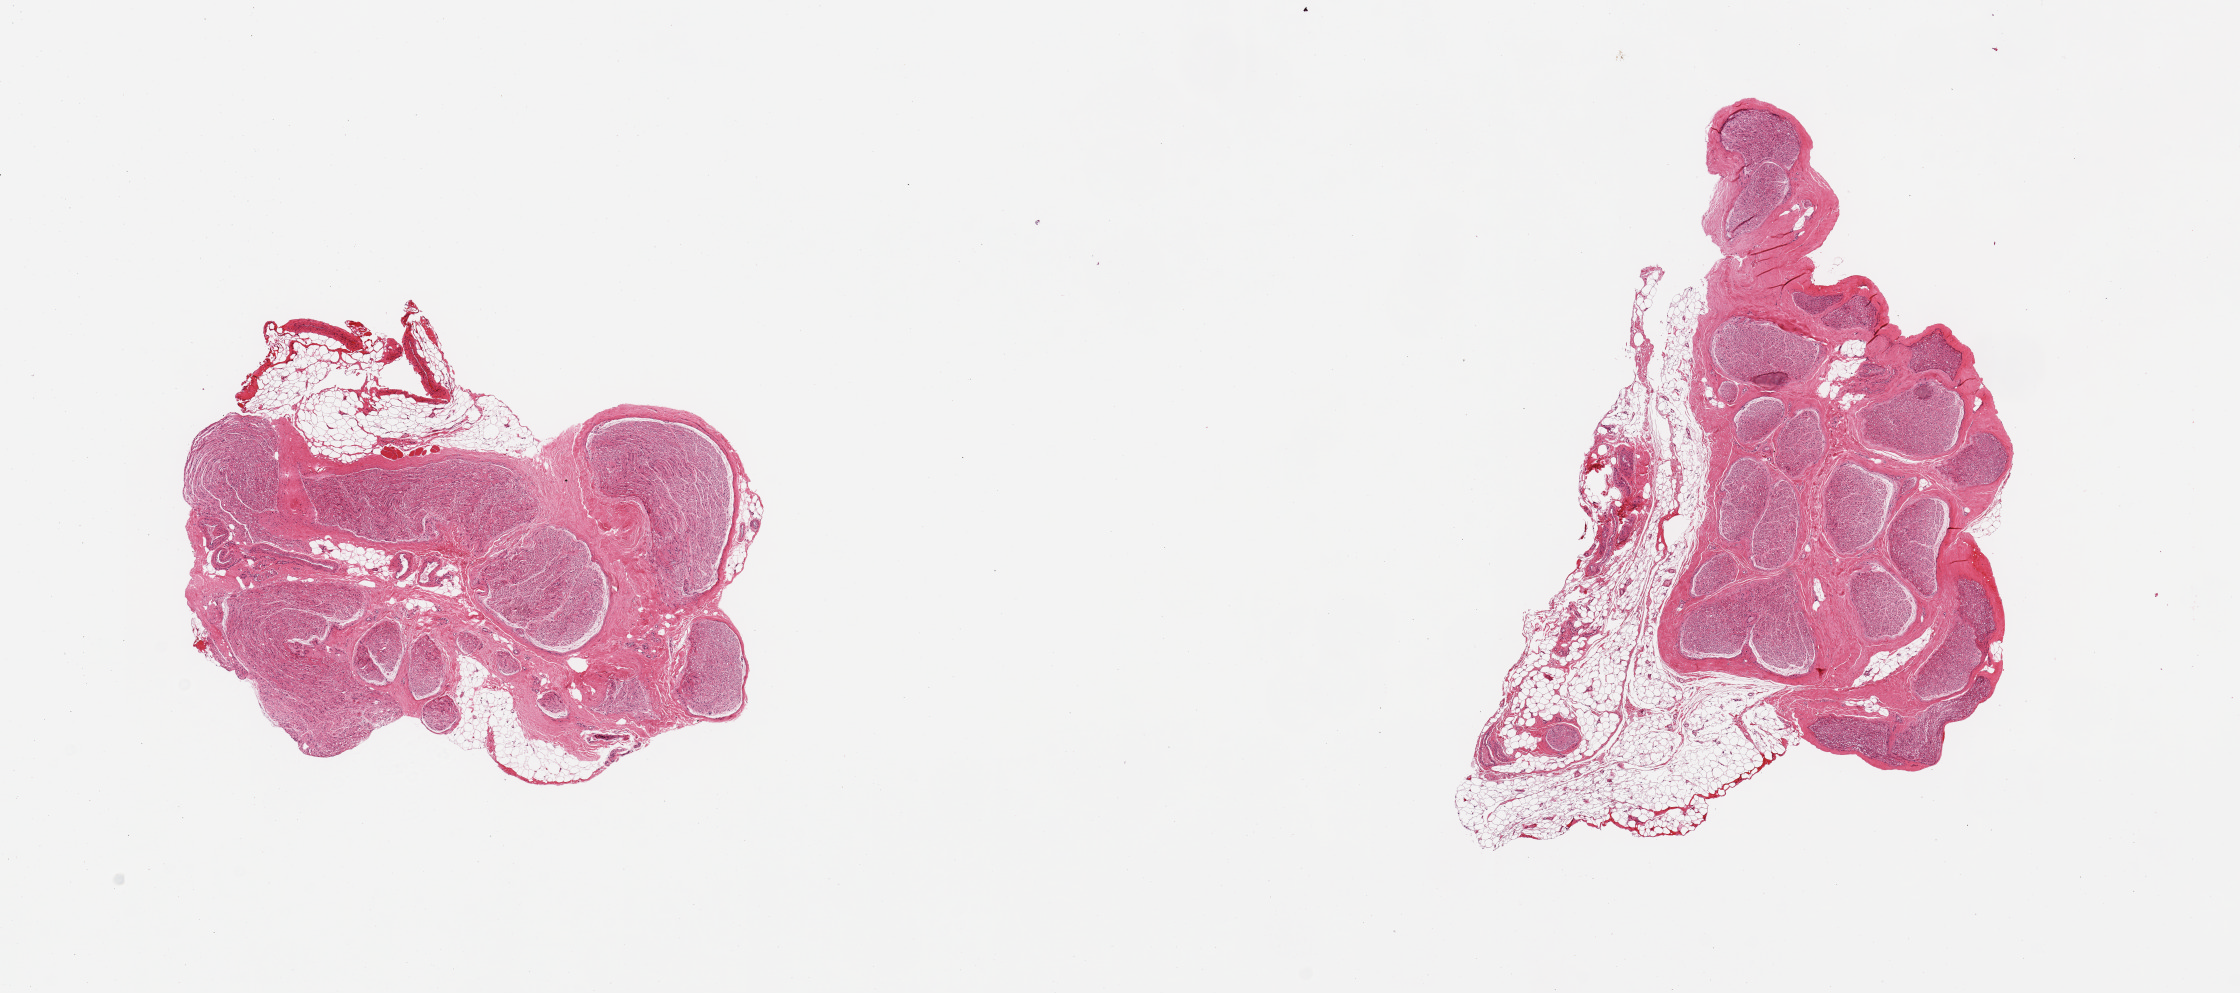
Whole-slide image, H&E stain, a low-resolution overview of the entire scanned area, about 17.7 x 7.9 mm, PAXgene-fixed paraffin-embedded (PFPE) section, sampled site (target tissue): tibial nerve, donor tissue sample.
Review note (as recorded): 2 pieces, trace nubbins of adherent fat, ~1-2mm.